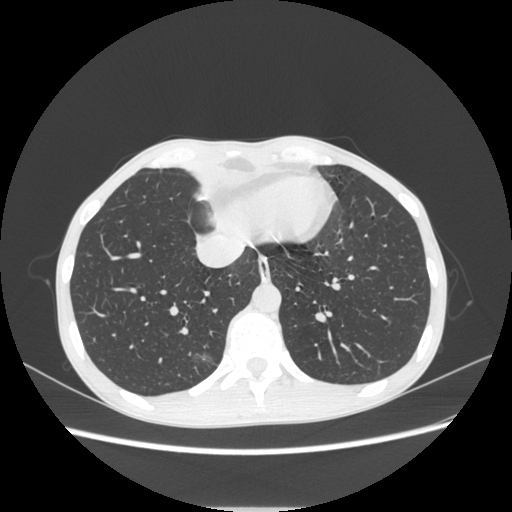
Chest CT, one axial slice; slice 82 of 272 in the series (ordered by position); reconstruction kernel STANDARD; 120 kVp; lung window (W 1500 / L -600 HU); 512 × 512 image matrix, field of view 350 × 350 mm. Patient: female, 51 years. Case-level facts recorded for this patient, not image findings: clinical TNM (as recorded): T1c N0 M0.
Structures marked on this image (bounding box drawn by a radiologist):
- lung tumour (recorded histology: adenocarcinoma): bounding box <184,344,219,374> (left, top, right, bottom; pixels)